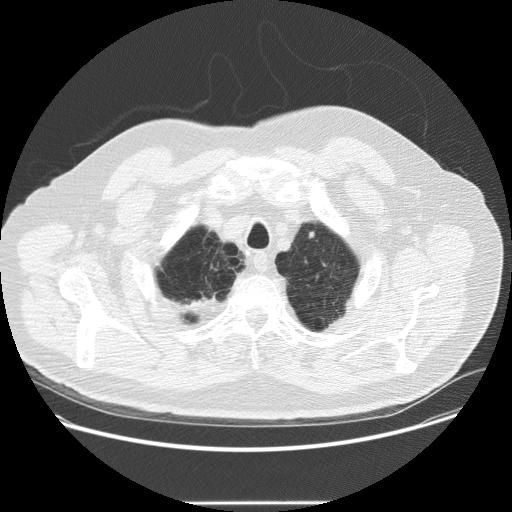
Axial slice from a low-dose chest CT screening exam. Second screening round (one year after baseline). Lung window (W 1500 / L -600 HU). Standard (soft-tissue) reconstruction kernel (STANDARD). 120 kVp. 512 × 512 image matrix. Male, age 64 years at enrolment. Current smoker at enrolment.
Expert reader's lesion annotation, box from (x=299, y=224) to (x=326, y=250) px. Reader record for this screening exam (exam-level; its link to the box is not recorded): non-calcified nodule or mass ≥4 mm, left upper lobe, 5 × 3 mm, smooth margins, soft tissue attenuation, pre-existing on the prior screen: no. Participant outcome: lung cancer diagnosed 300 days after this screen — adenocarcinoma, NOS, left upper lobe, poorly differentiated (G3), stage IA (AJCC 6th edition), 8 mm at pathology.